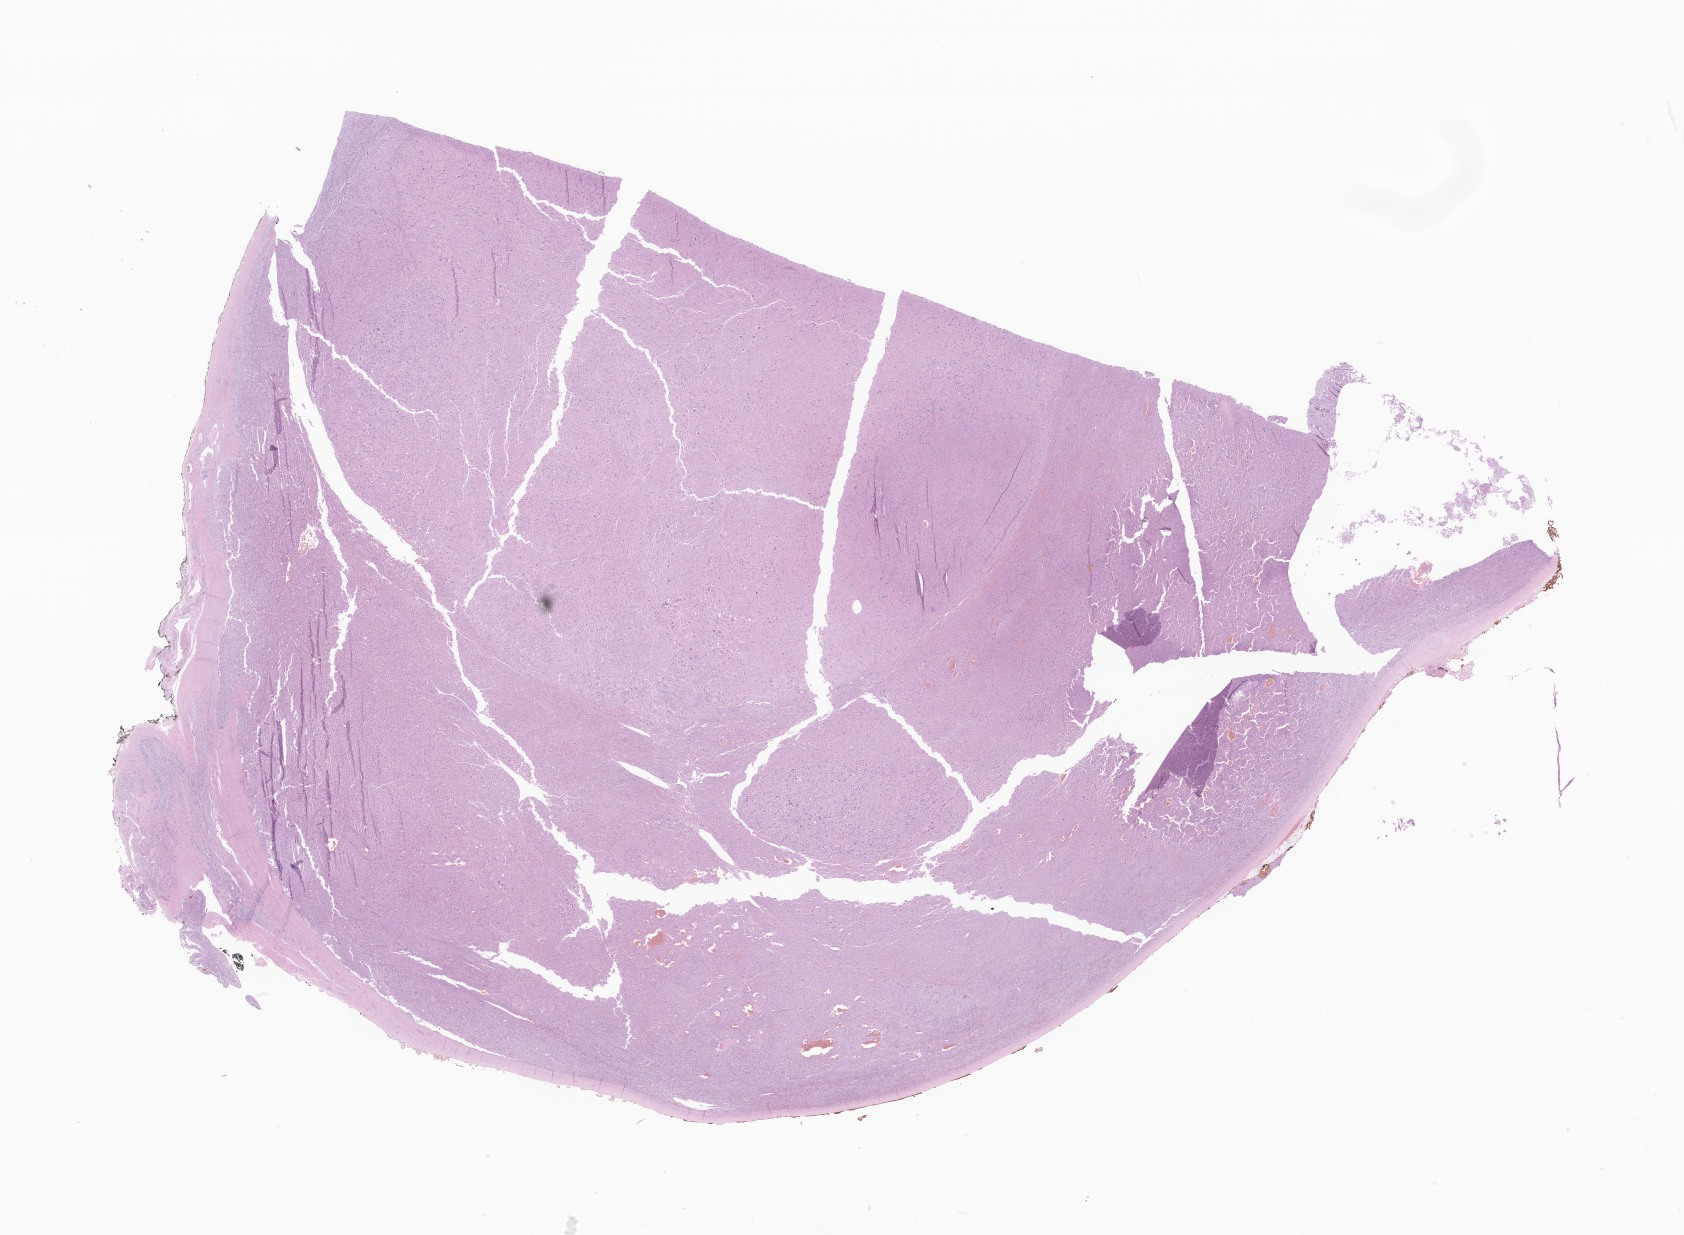
H&E whole-slide image of tumor tissue from the adrenal gland, low-resolution overview of the scanned area, about 28.4 x 20.8 mm; formalin-fixed, paraffin-embedded (FFPE) tissue. Patient: female, age 615 days (about 1.7 years).
Diagnosis: Adrenal cortical carcinoma.